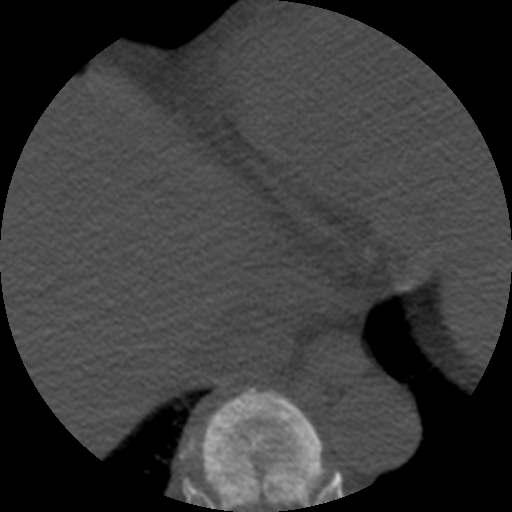
CT including the spine, one axial slice; slice 302 of 508 in the series (ordered by position); reconstruction kernel STANDARD; bone window (W 1800 / L 400 HU); 1.25 mm slice thickness; 512 × 512 image matrix, field of view 160 × 160 mm. Patient age 57 years. Case-level facts recorded for this patient, not image findings: primary cancer: prostate.
Outlined on this slice (semi-automatically segmented with operator editing):
- T8 vertebra: bounding box (x1, y1, x2, y2) in pixels: (181, 389, 324, 512)